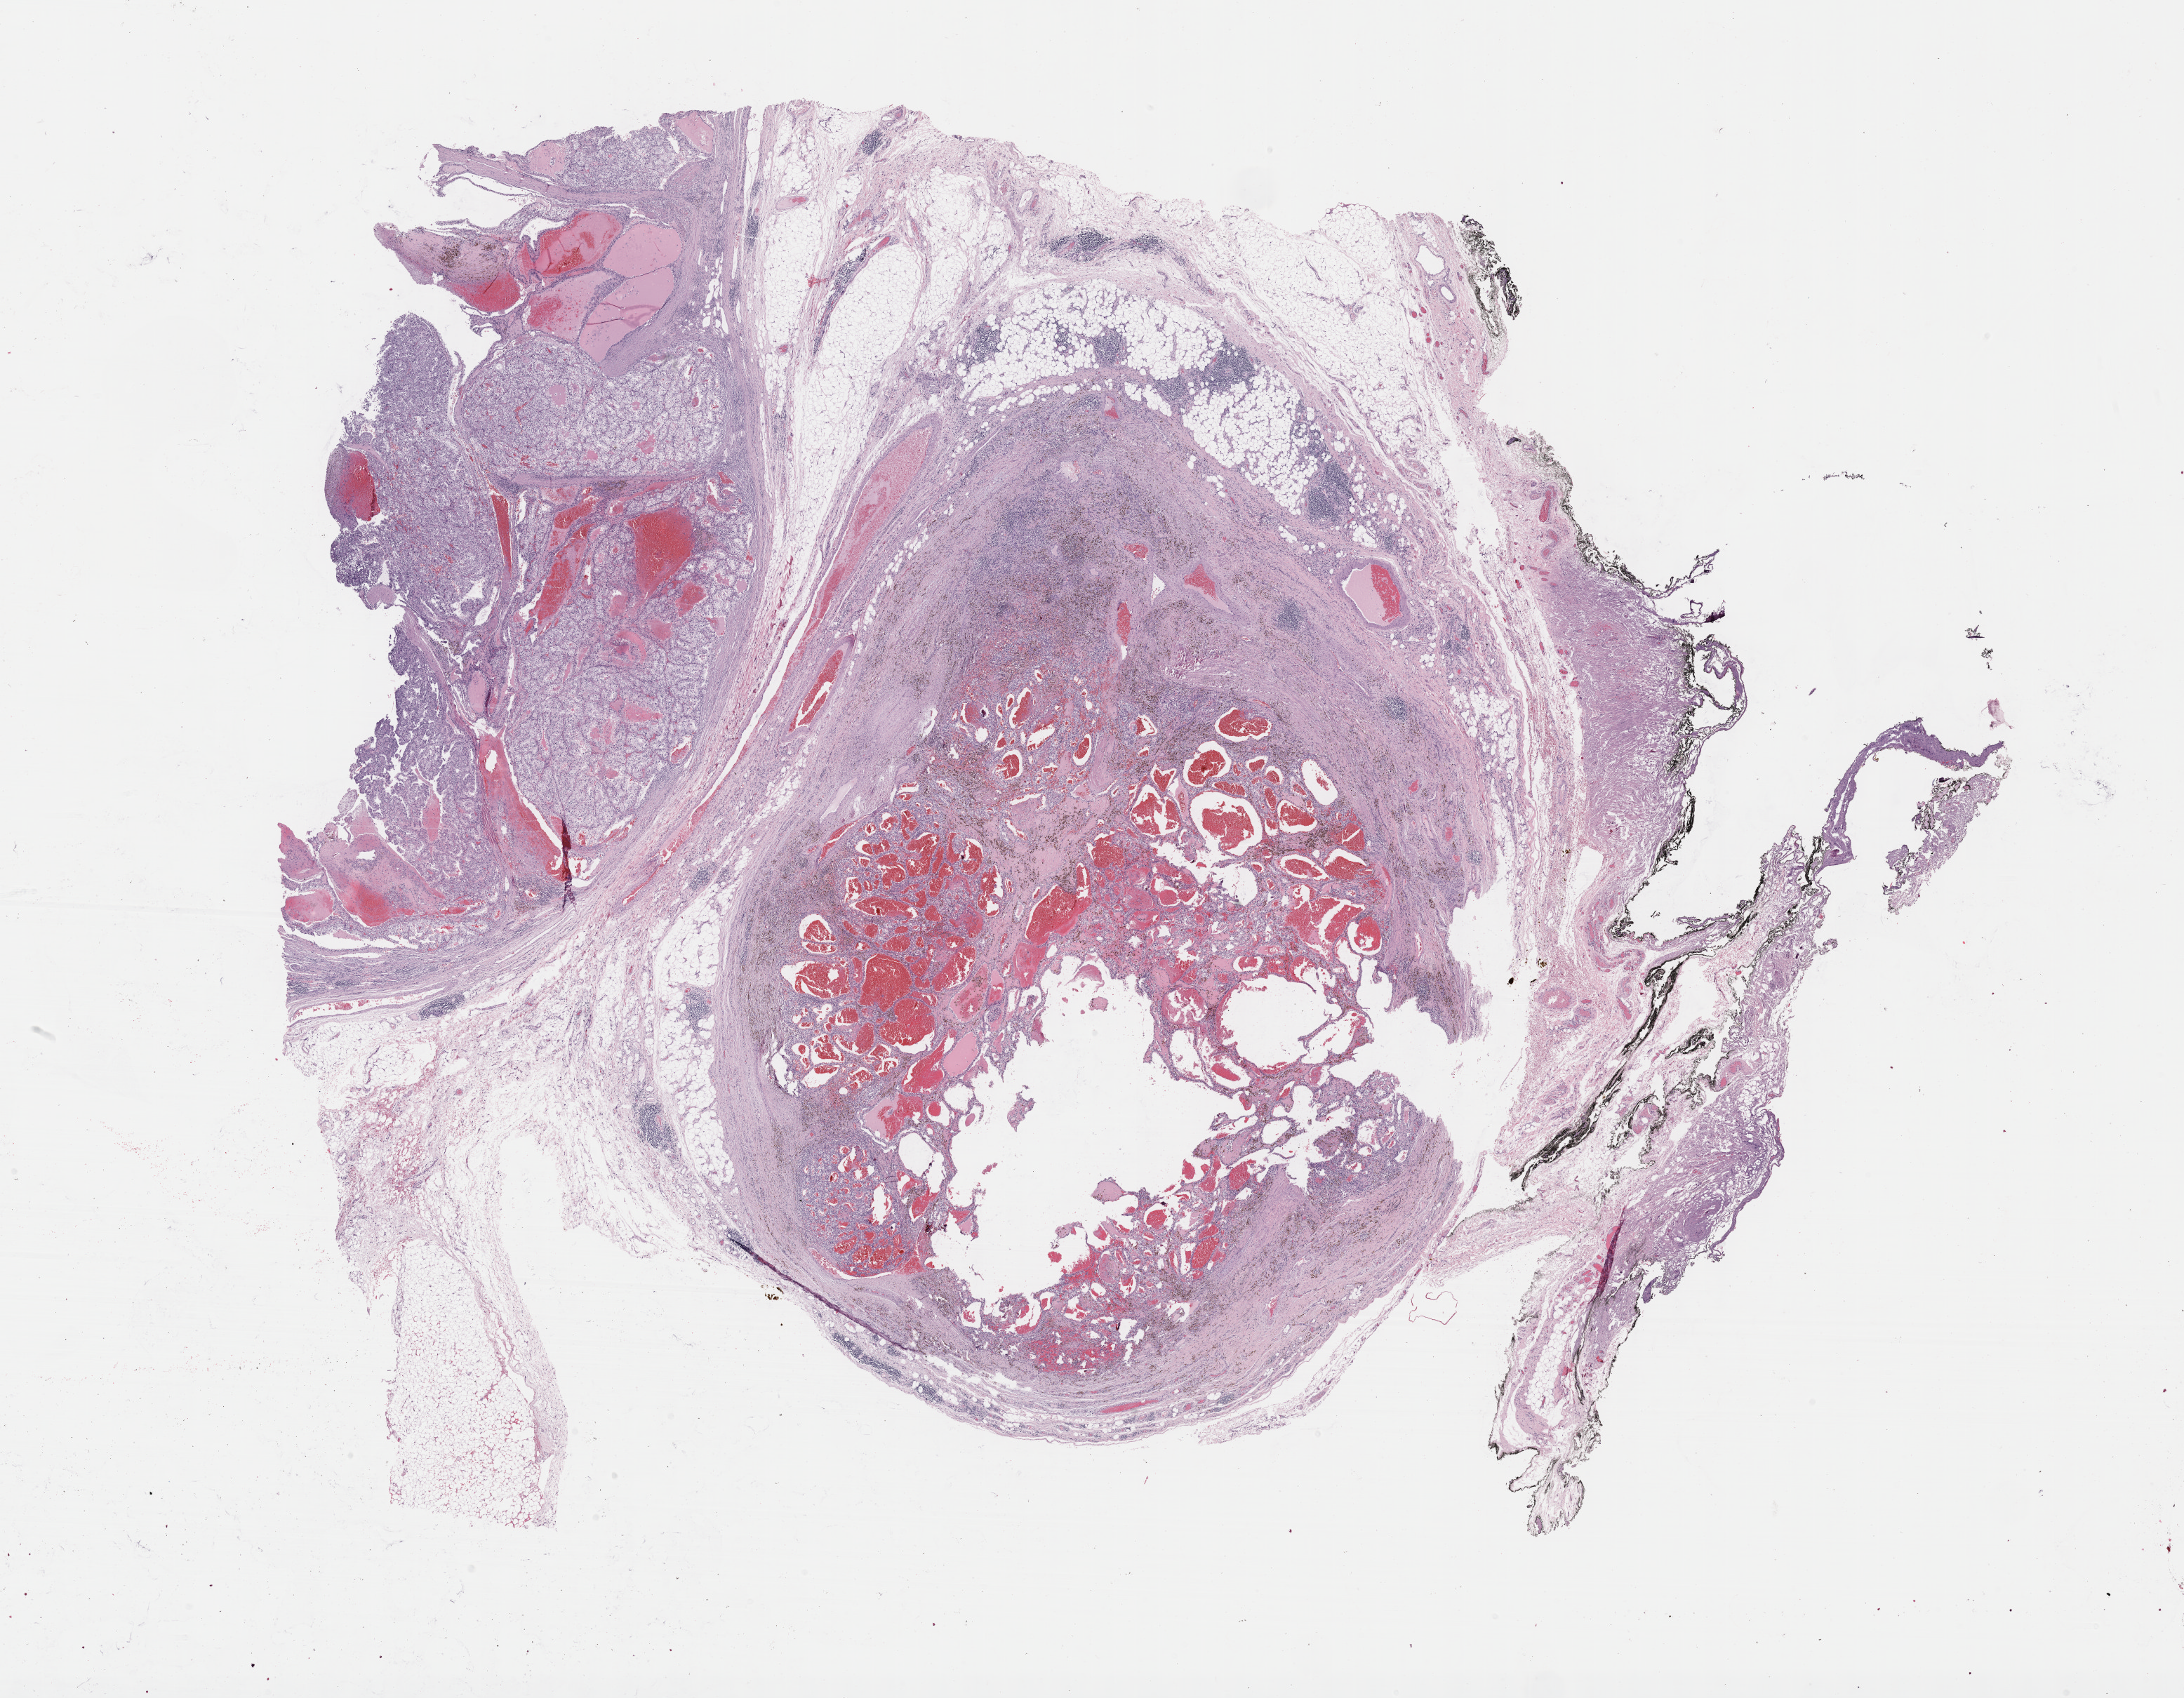
Whole-slide histology image, Hematoxylin and eosin (H&E) stained, low-resolution overview of the scanned area, about 25.2 x 19.6 mm, formalin-fixed paraffin-embedded (FFPE) diagnostic section, primary tumour sample from the kidney. Male, age 41 years at initial diagnosis. Histologic grade: G2 (moderately differentiated).
Laterality: left. Diagnosis: Clear cell adenocarcinoma, NOS.